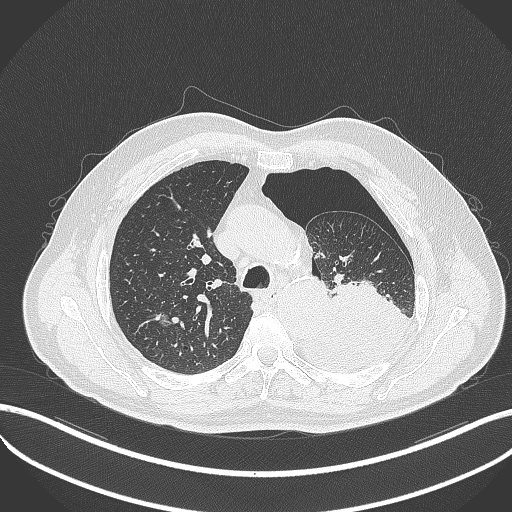
Chest CT, one axial slice. Slice 365 of 464 in the series (ordered by position). Lung window (W 1500 / L -600 HU). 512 × 512 image matrix, field of view 400 × 400 mm. Patient: male, 76 years. From the clinical record (not read from this slice): clinical TNM (as recorded): T3 N0 M1b.
Structures marked on this image (bounding box drawn by a radiologist):
- lung tumour (recorded histology: adenocarcinoma): bounding box <305,281,412,375> (left, top, right, bottom; pixels)